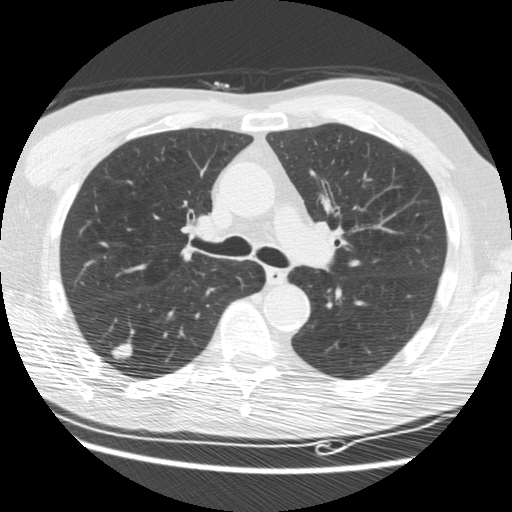
Low-dose screening chest CT, one axial slice. Slice 110 of 176 in the series (ordered by position). 120 kVp. Lung window (W 1500 / L -600 HU). 512 × 512 image matrix, field of view 347 × 347 mm.
Structures marked on this image (outlined manually by an expert reader):
- lesion 1 (tumor, lower lobe of right lung): box from (x=111, y=343) to (x=132, y=360) px